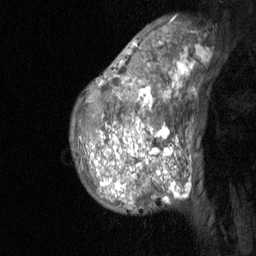
Breast MRI (dynamic contrast-enhanced), one sagittal slice. Position 45 of 64 along the scan axis. Dynamic contrast-enhanced study with each time point stored as its own series, time point 2 of 3 at this slice position (early post-contrast, ordered by acquisition time). 1.5 T. TE 4.8 ms, TR 27 ms. 2 mm slice thickness. 256 × 256 image matrix, field of view 180 × 180 mm. Female patient, age 36 years. Case-level facts recorded for this patient, not image findings: setting: breast cancer imaged before/during neoadjuvant chemotherapy; receptor status: HR-positive, HER2-negative.
Structures marked on this image (semi-automatically segmented with operator editing):
- analysis volume of interest (the breast-tissue region the enhancement analysis was run in; not a lesion): bounding box (x1, y1, x2, y2) in pixels: (70, 17, 197, 215)
- tumour enhancement mask (voxels above the 90 % enhancement threshold inside the analysis volume of interest): (100, 60, 183, 202)